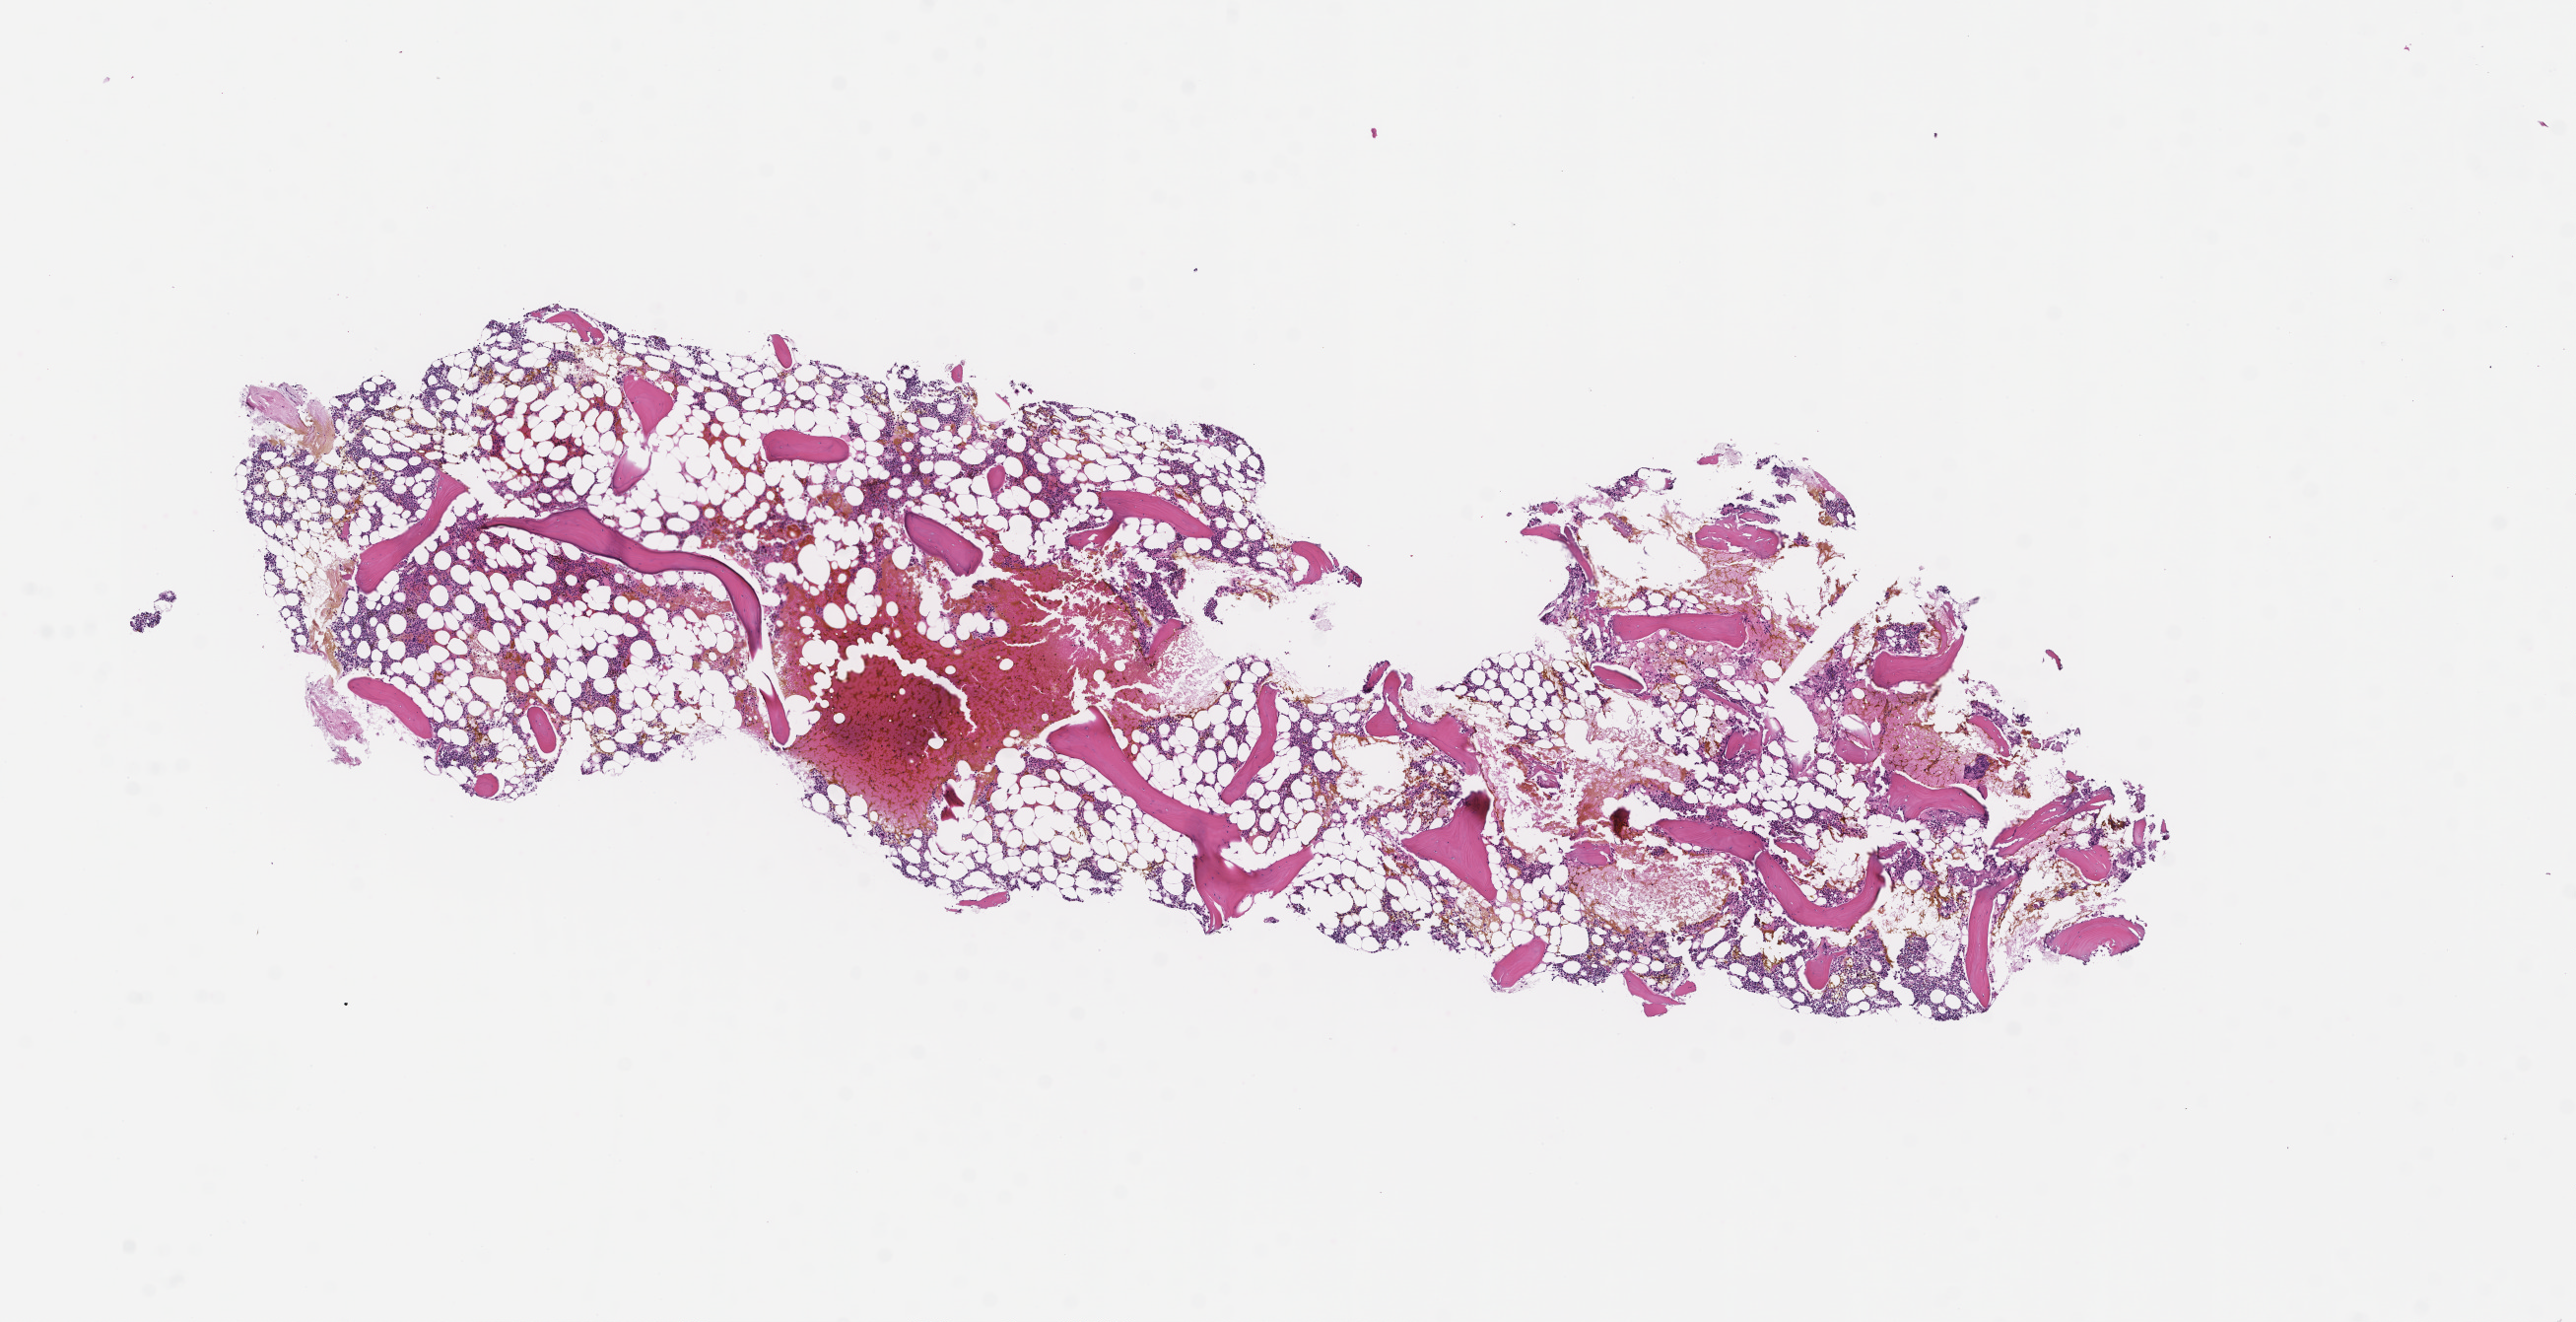
Whole-slide image, hematoxylin and eosin (H&E) stain — a low-resolution overview of the entire scanned area, about 10.6 x 5.4 mm. Formalin-fixed paraffin-embedded section. Tissue site: bone marrow. Specimen time point: archival tissue. Patient sex: male.
This section: primary tumor. Diagnosis: Plasma Cell Myeloma.